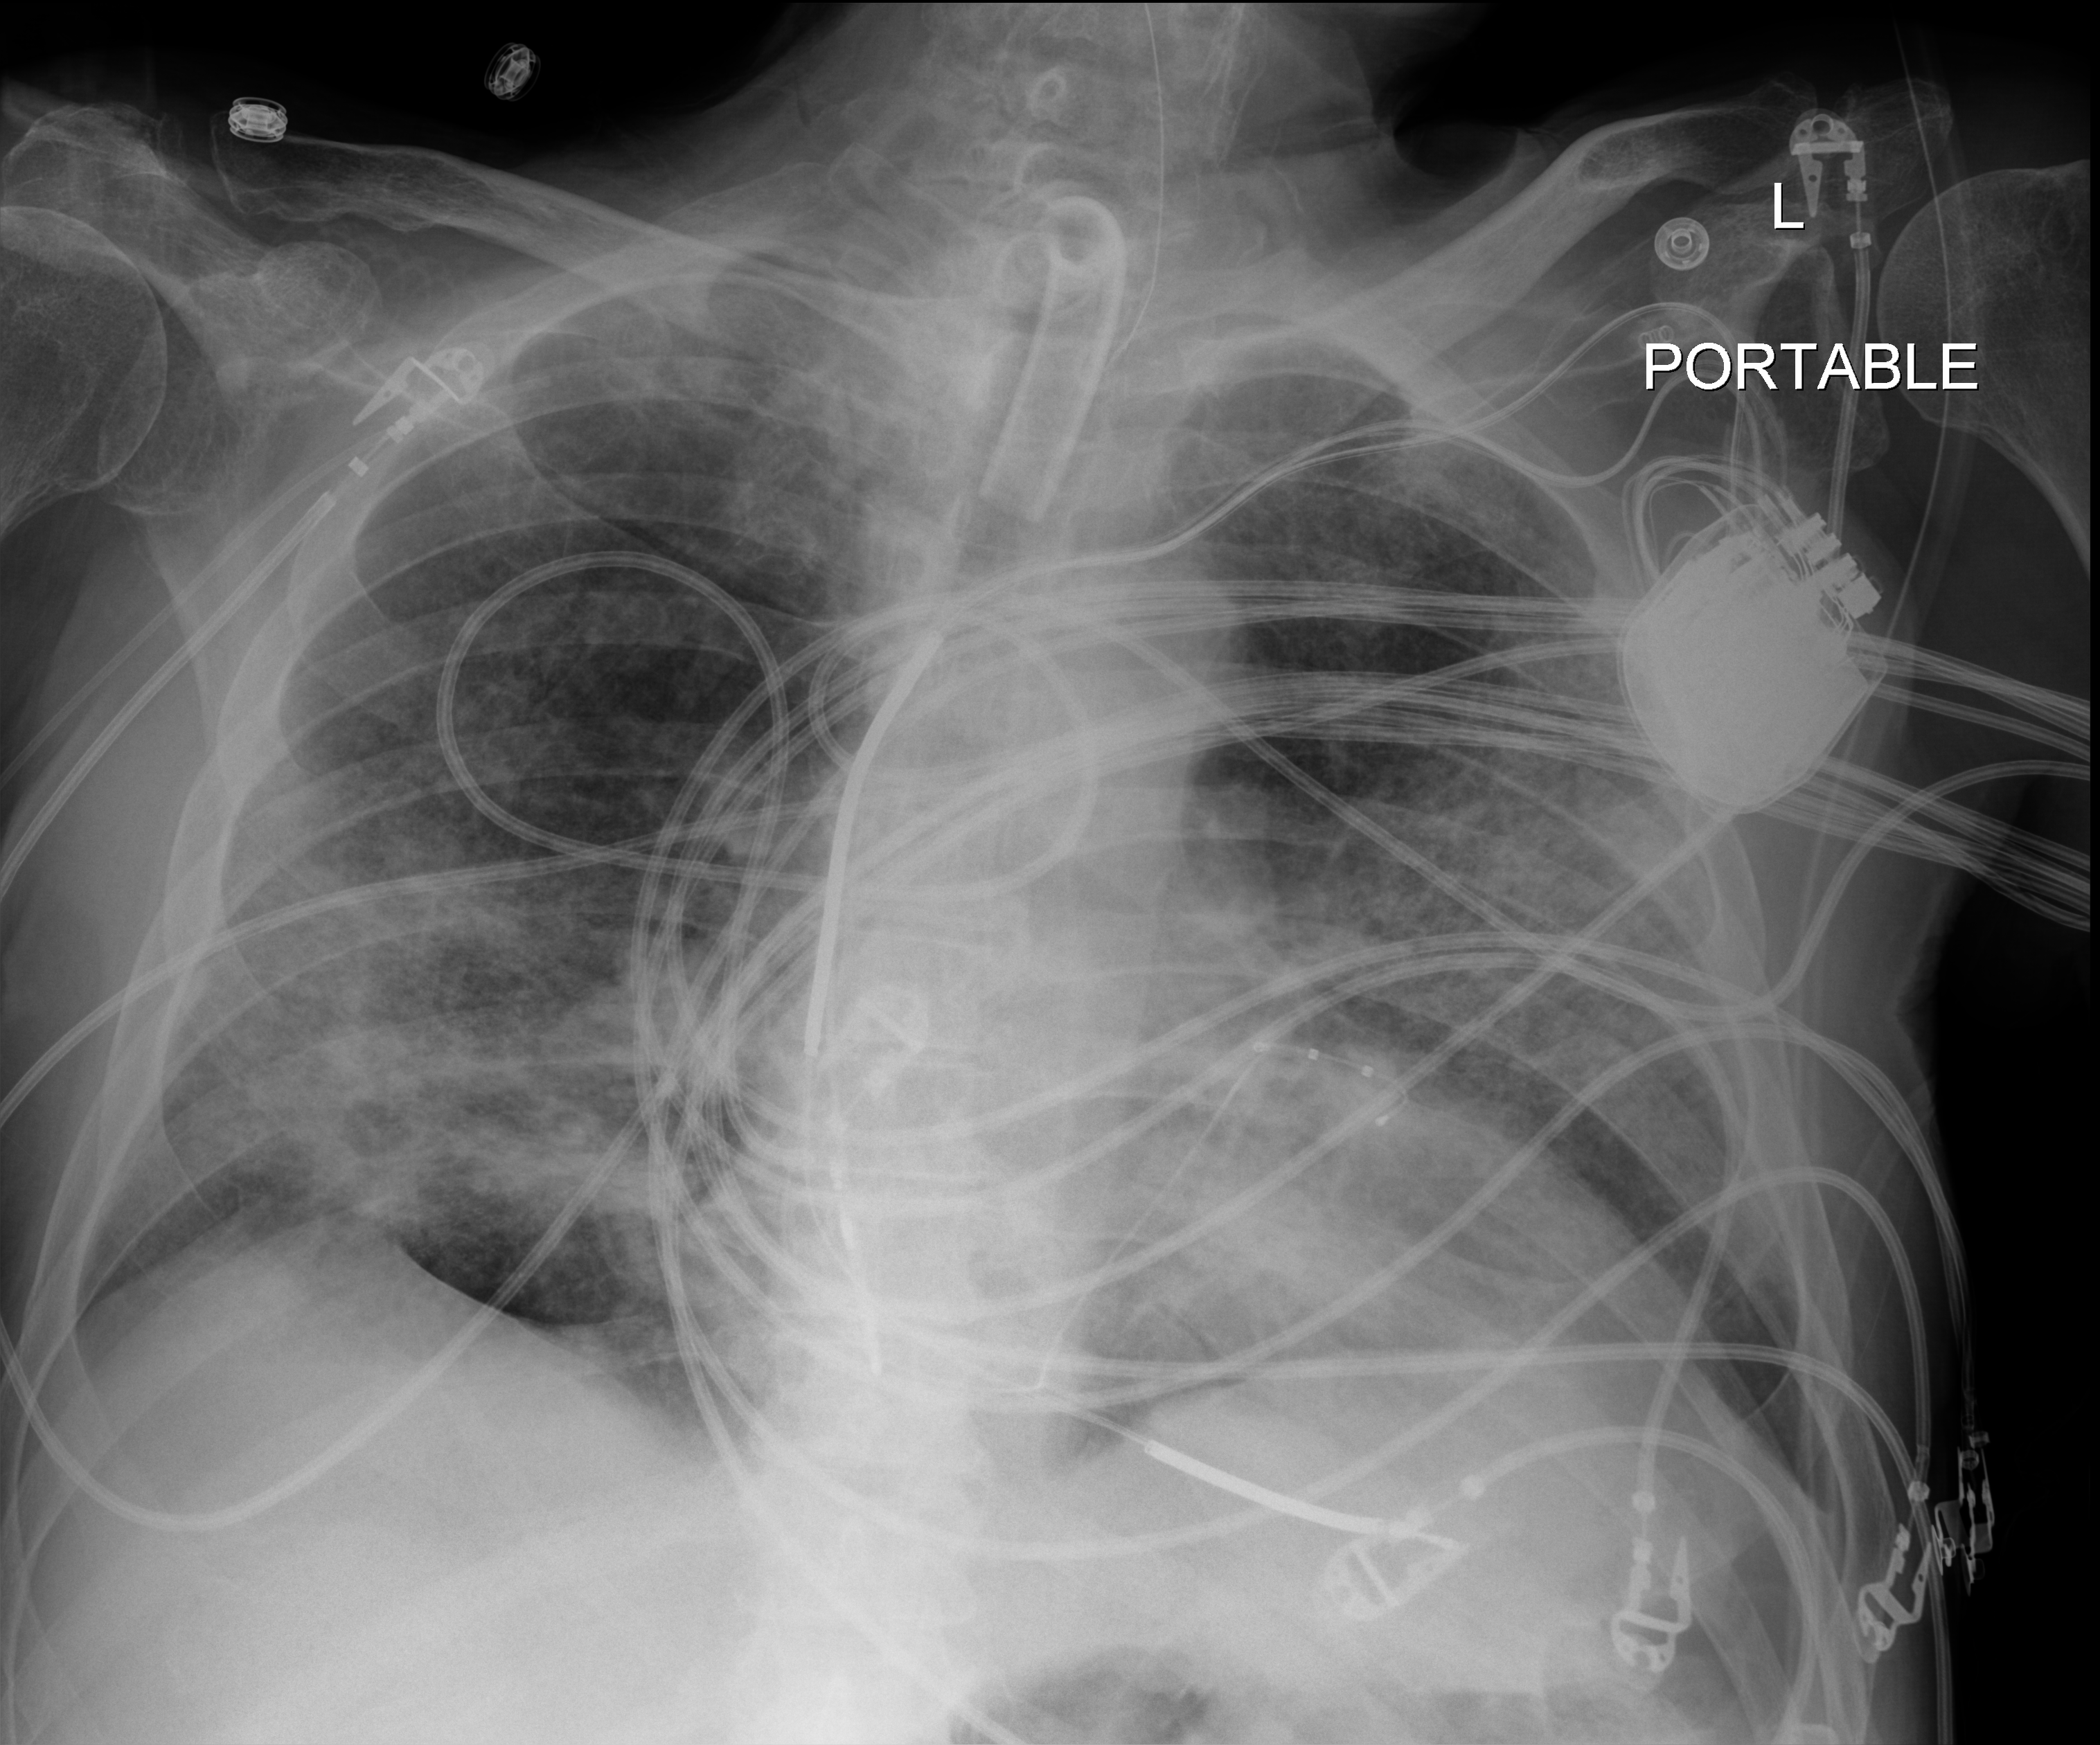
Portable chest radiograph. Patient hospitalised with COVID-19; male, aged 60–74 years.
Hospital-stay facts (about this admission, not read from this image; timing relative to this image not recorded): admitted to intensive care during this hospital stay: yes; smoking status (admission record): former.